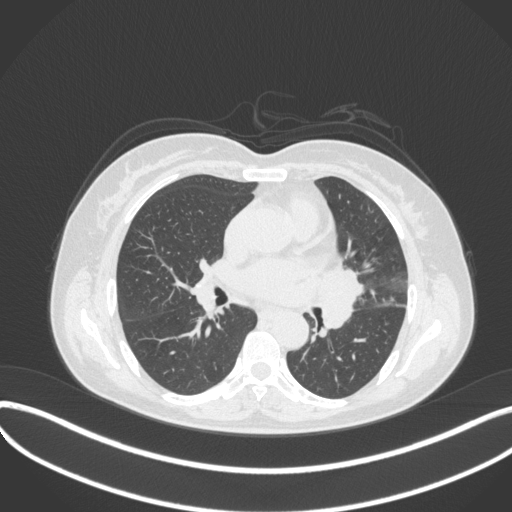
Chest CT, one axial slice; slice 185 of 373 in the series (ordered by position); 120 kVp; lung window (W 1500 / L -600 HU); 1 mm slice thickness; 512 × 512 image matrix, field of view 400 × 400 mm. Female patient, age 54 years. Case-level facts recorded for this patient, not image findings: clinical TNM (as recorded): T2a N1 M0; histopathological grade: G3.
Structures marked on this image (rectangle marked by the reading radiologist):
- lung tumour (recorded histology: small cell carcinoma): bounding box [x1, y1, x2, y2] px = [312, 261, 366, 337]